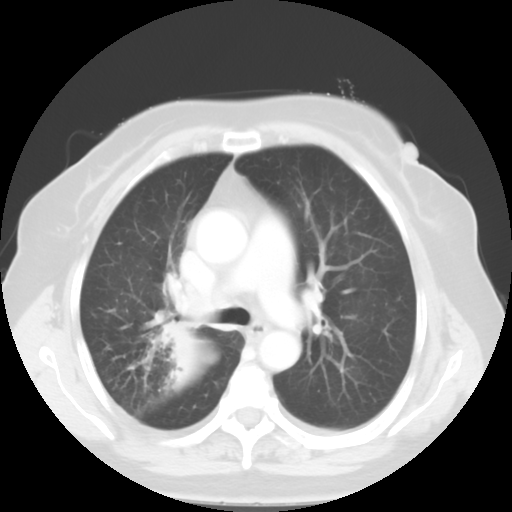
Chest CT, one axial slice; 120 kVp; lung window (W 1500 / L -600 HU); 5 mm slice thickness; 512 × 512 image matrix. Patient: female, 81 years. Case-level facts recorded for this patient, not image findings: clinical TNM (as recorded): T4 N3 M1b.
Outlined on this slice (bounding box drawn by a radiologist):
- lung tumour (recorded histology: adenocarcinoma): bounding box [x1, y1, x2, y2] px = [149, 314, 202, 383]